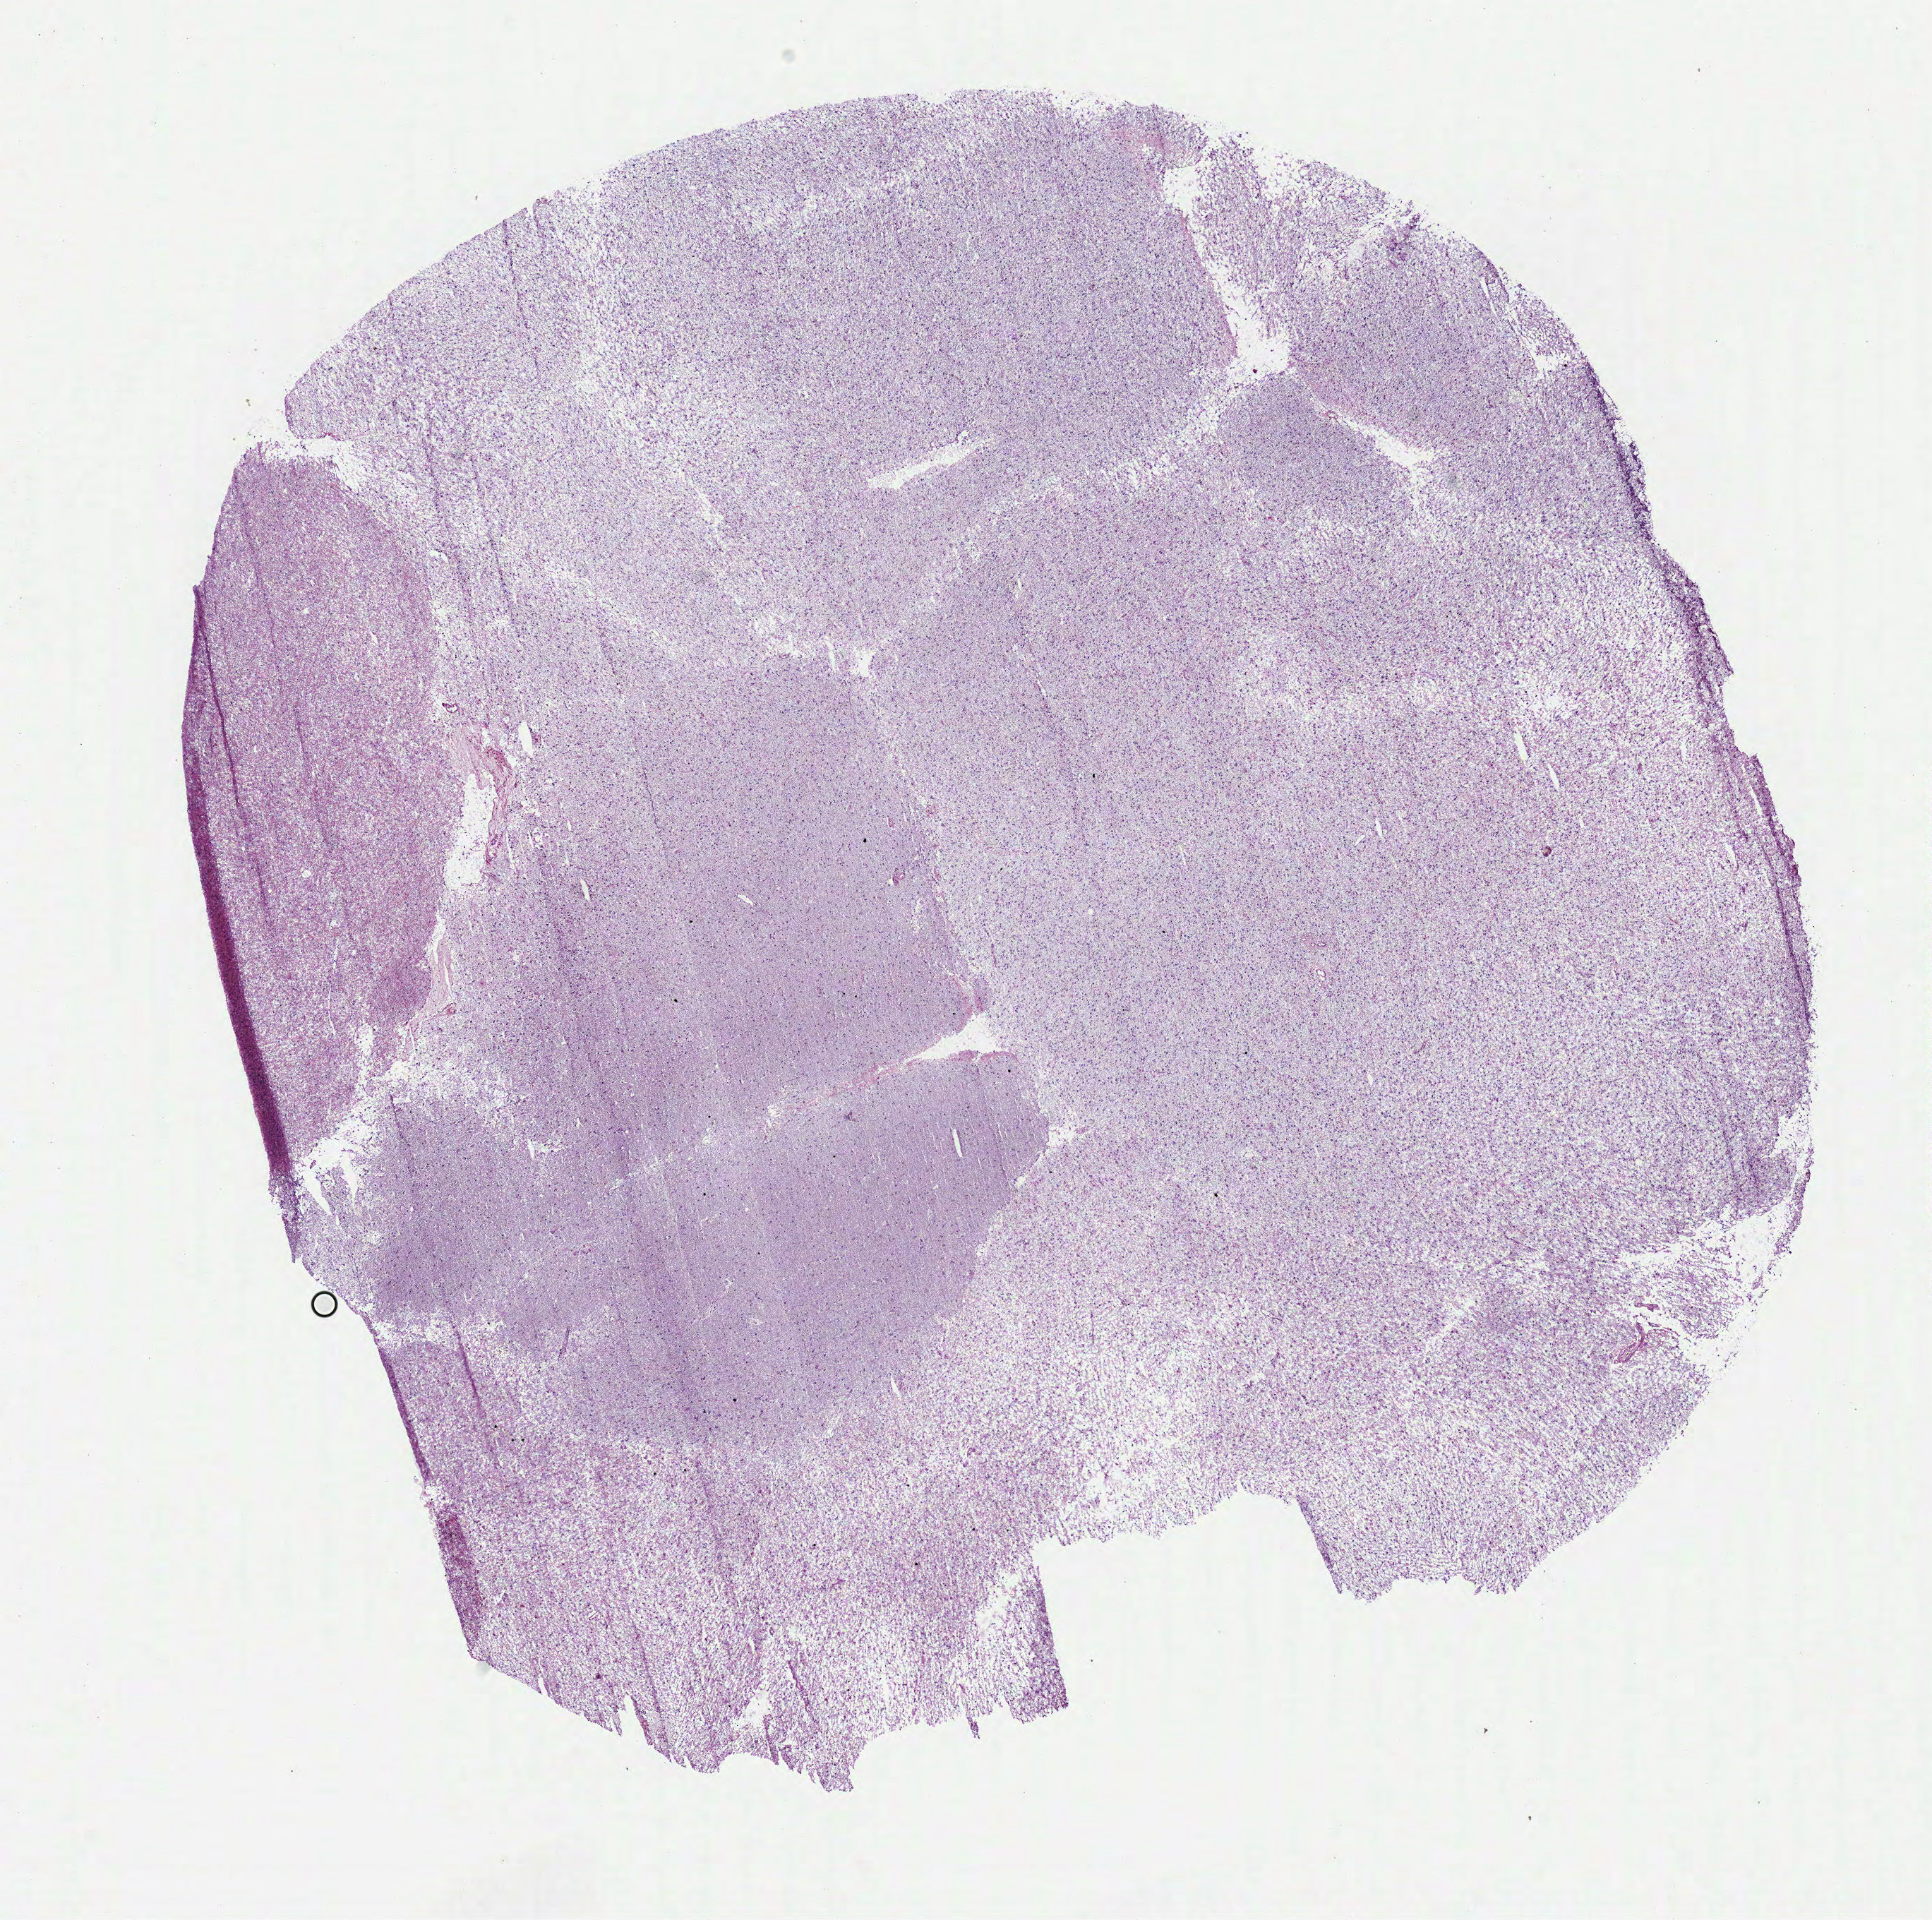
Digitized H&E-stained tissue section (whole slide), shown as a low-resolution overview of the whole scanned area (about 10.8 x 10.7 mm, slide scanned at 40x); frozen section; primary tumour sample from the brain. Male patient; age at initial diagnosis 29 years. Histologic grade: G2 (moderately differentiated). Slide review estimates, as recorded: tumour cells 100%, tumour nuclei 70%, normal cells 0%, stromal cells 0%, necrosis 0%.
Diagnosis: Mixed glioma. Laterality: left.